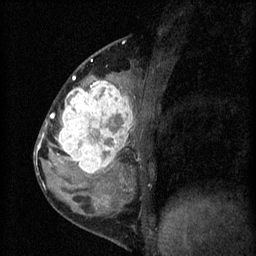
Breast MRI (dynamic contrast-enhanced), one sagittal slice; 3 images stored at this slice position (order not interpretable as contrast timing); 1.5 T; TE 4.2 ms, TR 8.2 ms; 2 mm slice thickness; 256 × 256 image matrix, field of view 180 × 180 mm. Female patient, age 37 years.
Outlined on this slice (semi-automatic segmentation, software-assisted and operator-edited):
- analysis volume of interest (the breast-tissue region the enhancement analysis was run in; not a lesion): box from (x=53, y=78) to (x=140, y=181) px
- tumour enhancement mask (voxels above the 70 % enhancement threshold inside the analysis volume of interest): (x=56, y=78)–(x=133, y=173)